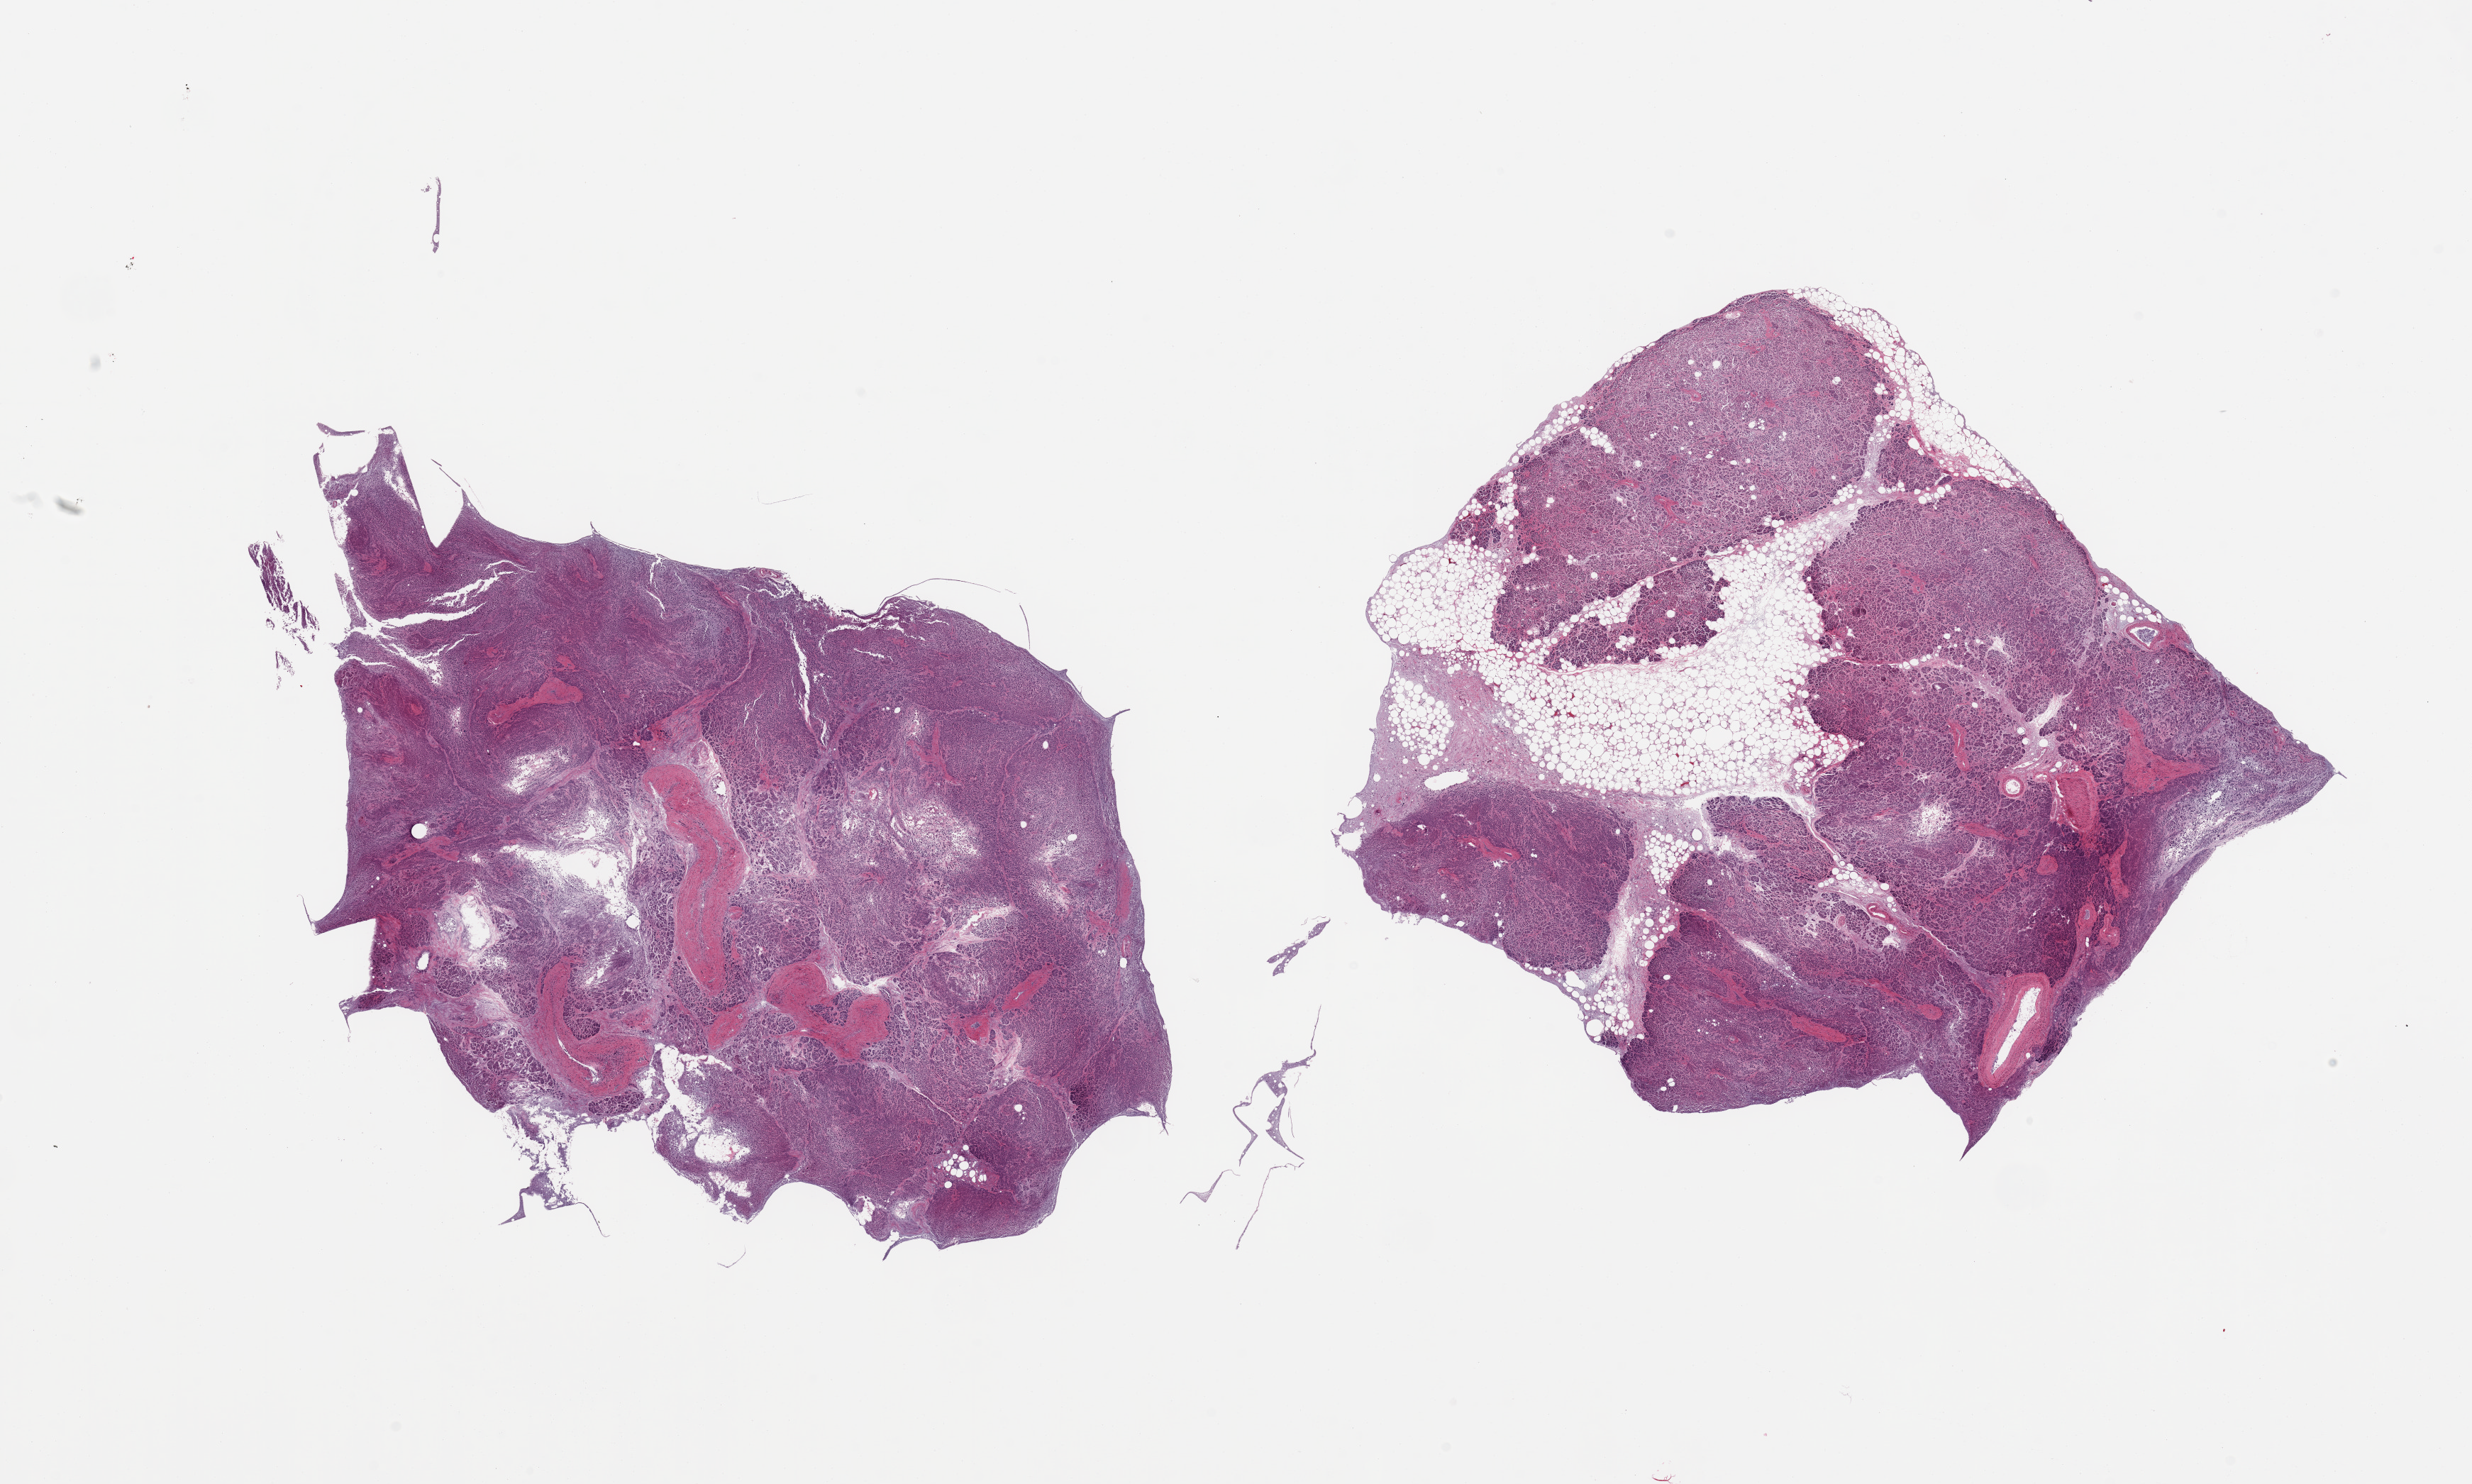
Digitized haematoxylin and eosin-stained section — whole scanned area (about 27.6 x 16.5 mm, slide scanned at 20x) shown as a low-resolution overview, PAXgene-fixed, paraffin-embedded tissue, section of pancreas (target tissue), tissue donor sample.
* pathologist's review note for this sample: 2 pieces; severe autolysis; 30% and 10% internal fat; thick walled vessel